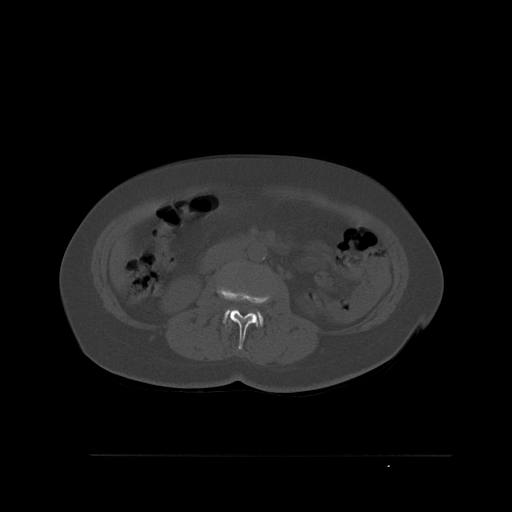
CT including the spine, one axial slice; slice 240 of 527 in the series (ordered by position); bone window (W 1800 / L 400 HU); 512 × 512 image matrix. Female patient, age 73 years. From the clinical record (not read from this slice): primary cancer: breast; vertebrae with lytic lesions (as recorded): L2.
Structures marked on this image (semi-automatic segmentation, software-assisted and operator-edited):
- L2 vertebra: bounding box (x1, y1, x2, y2) in pixels: (222, 288, 267, 350)
- L3 vertebra: (223, 309, 264, 326)
- L4 vertebra: (251, 311, 259, 325)